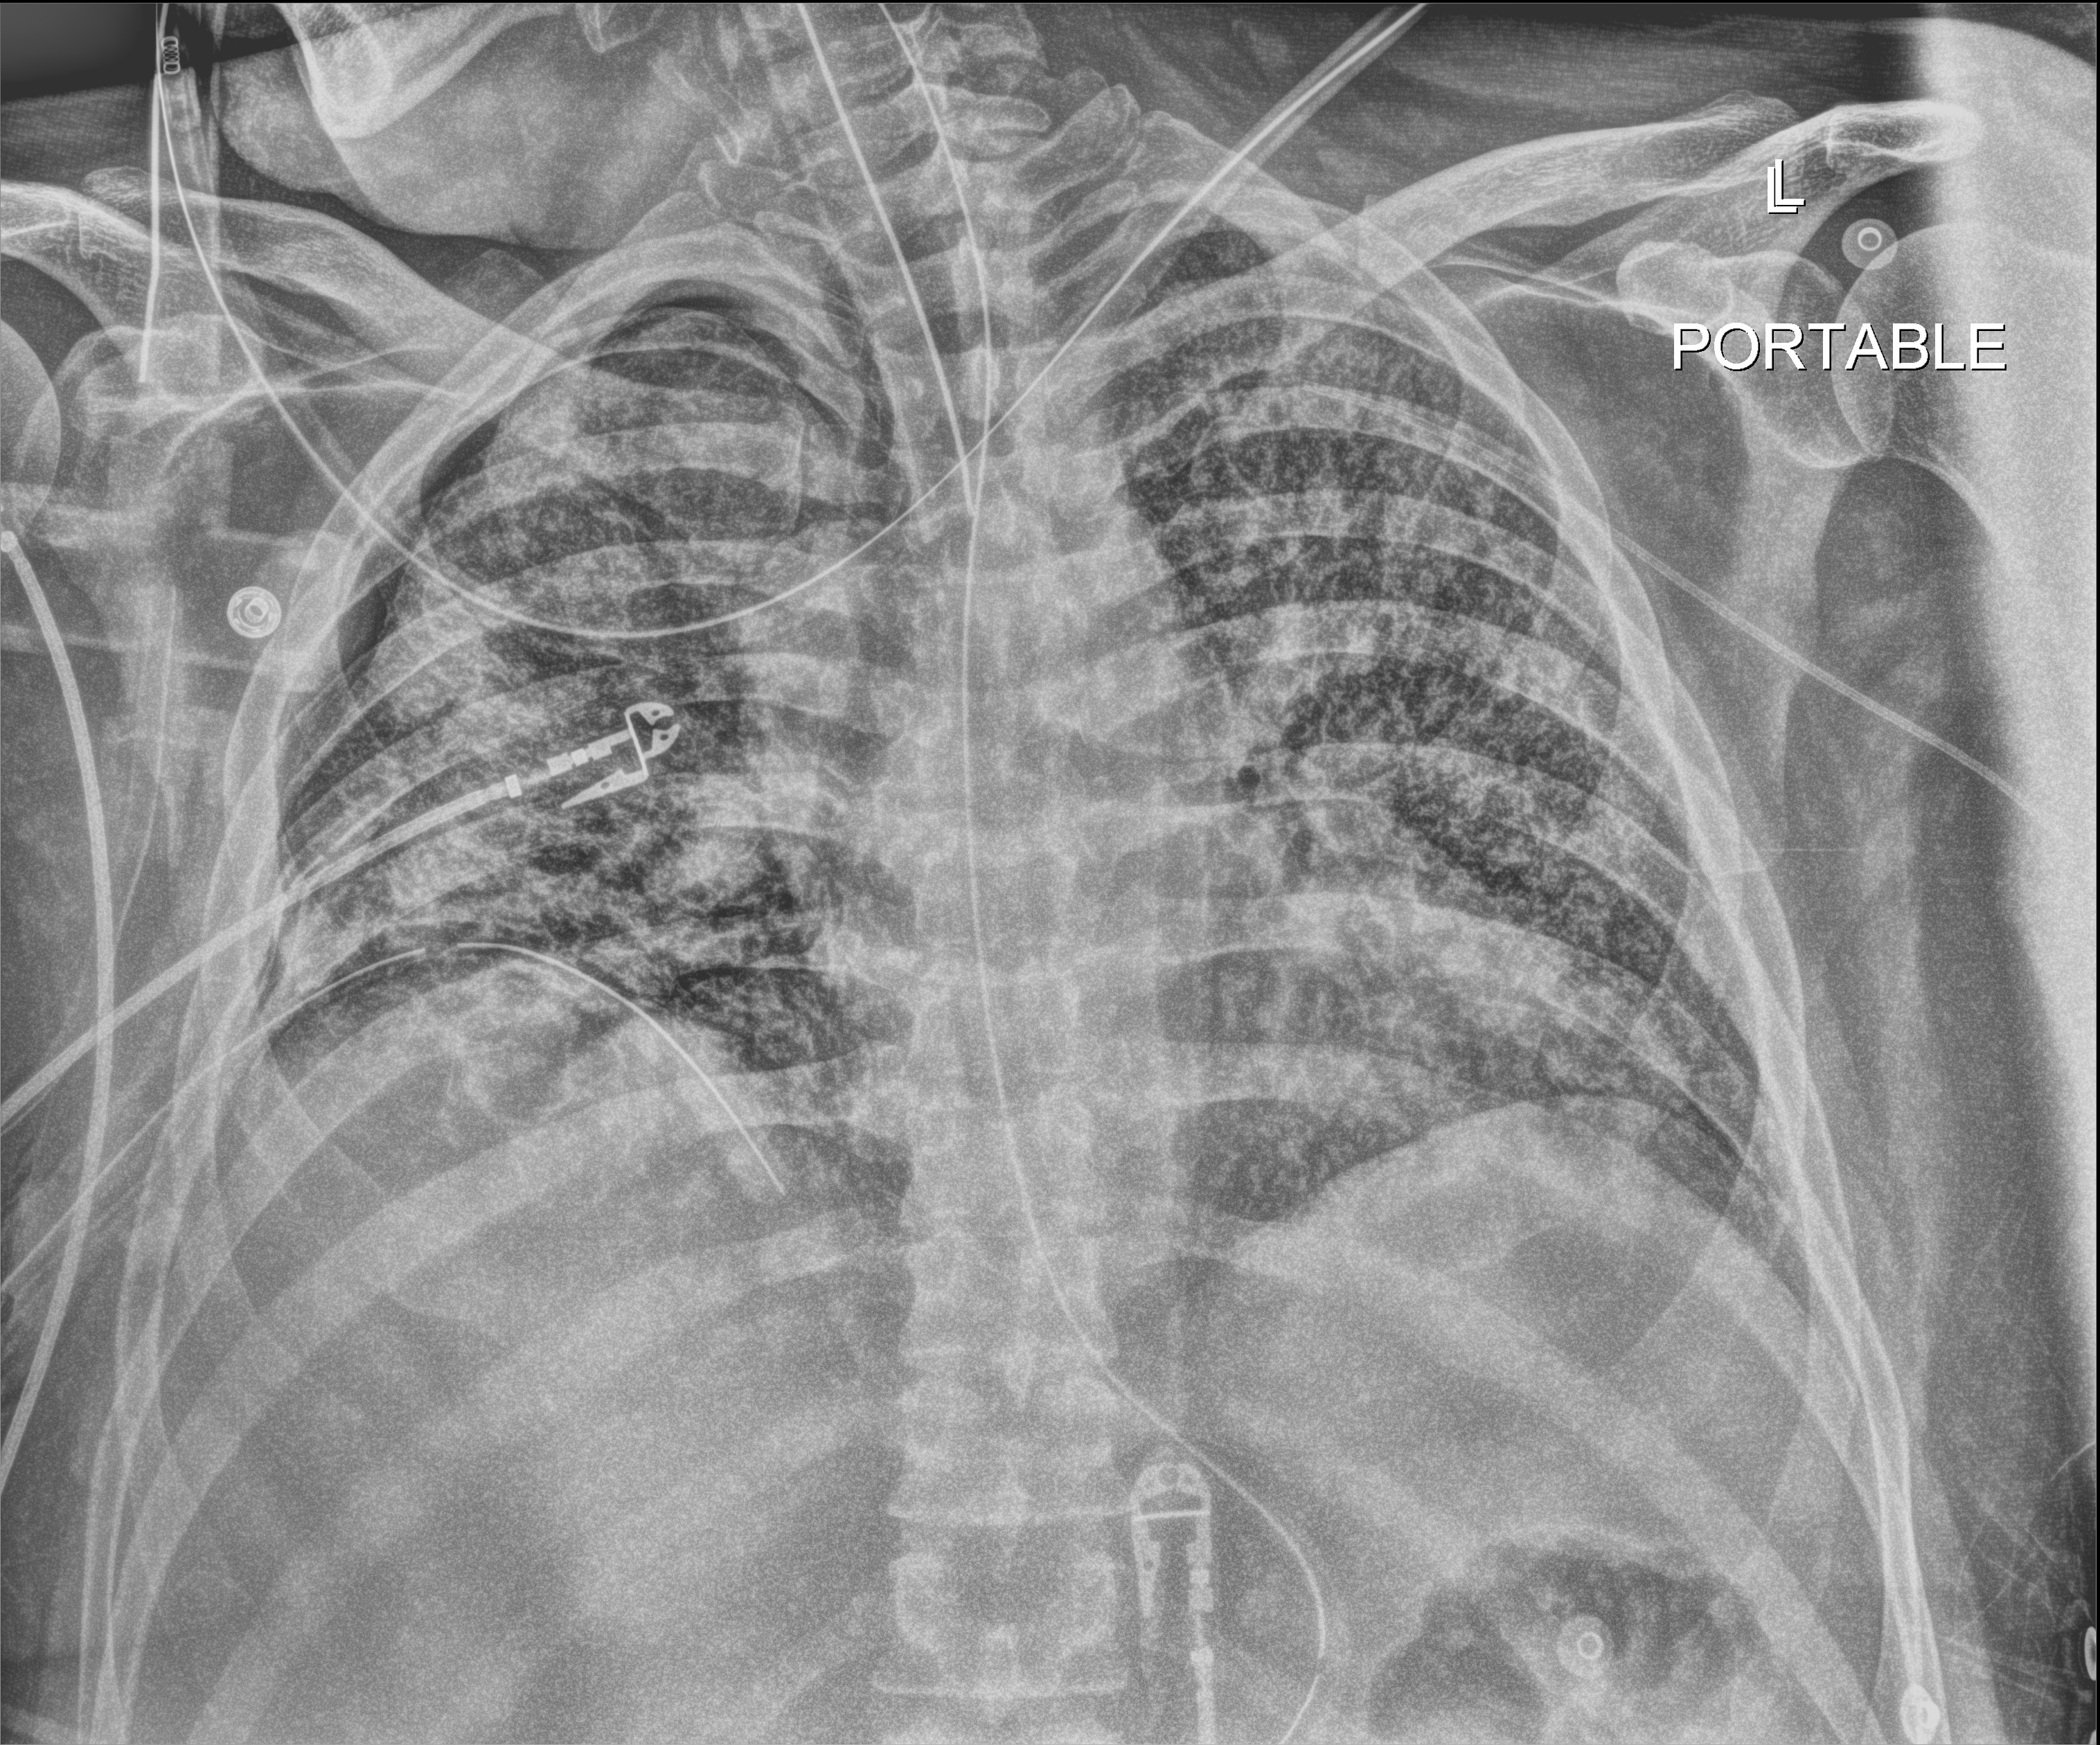
Bedside chest radiograph (digital radiography); anteroposterior (AP) projection. Patient hospitalised with COVID-19; male, aged 18–59 years.
Hospital-stay facts (about this admission, not read from this image; timing relative to this image not recorded): mechanically ventilated during this hospital stay: yes; COPD (admission record): no.